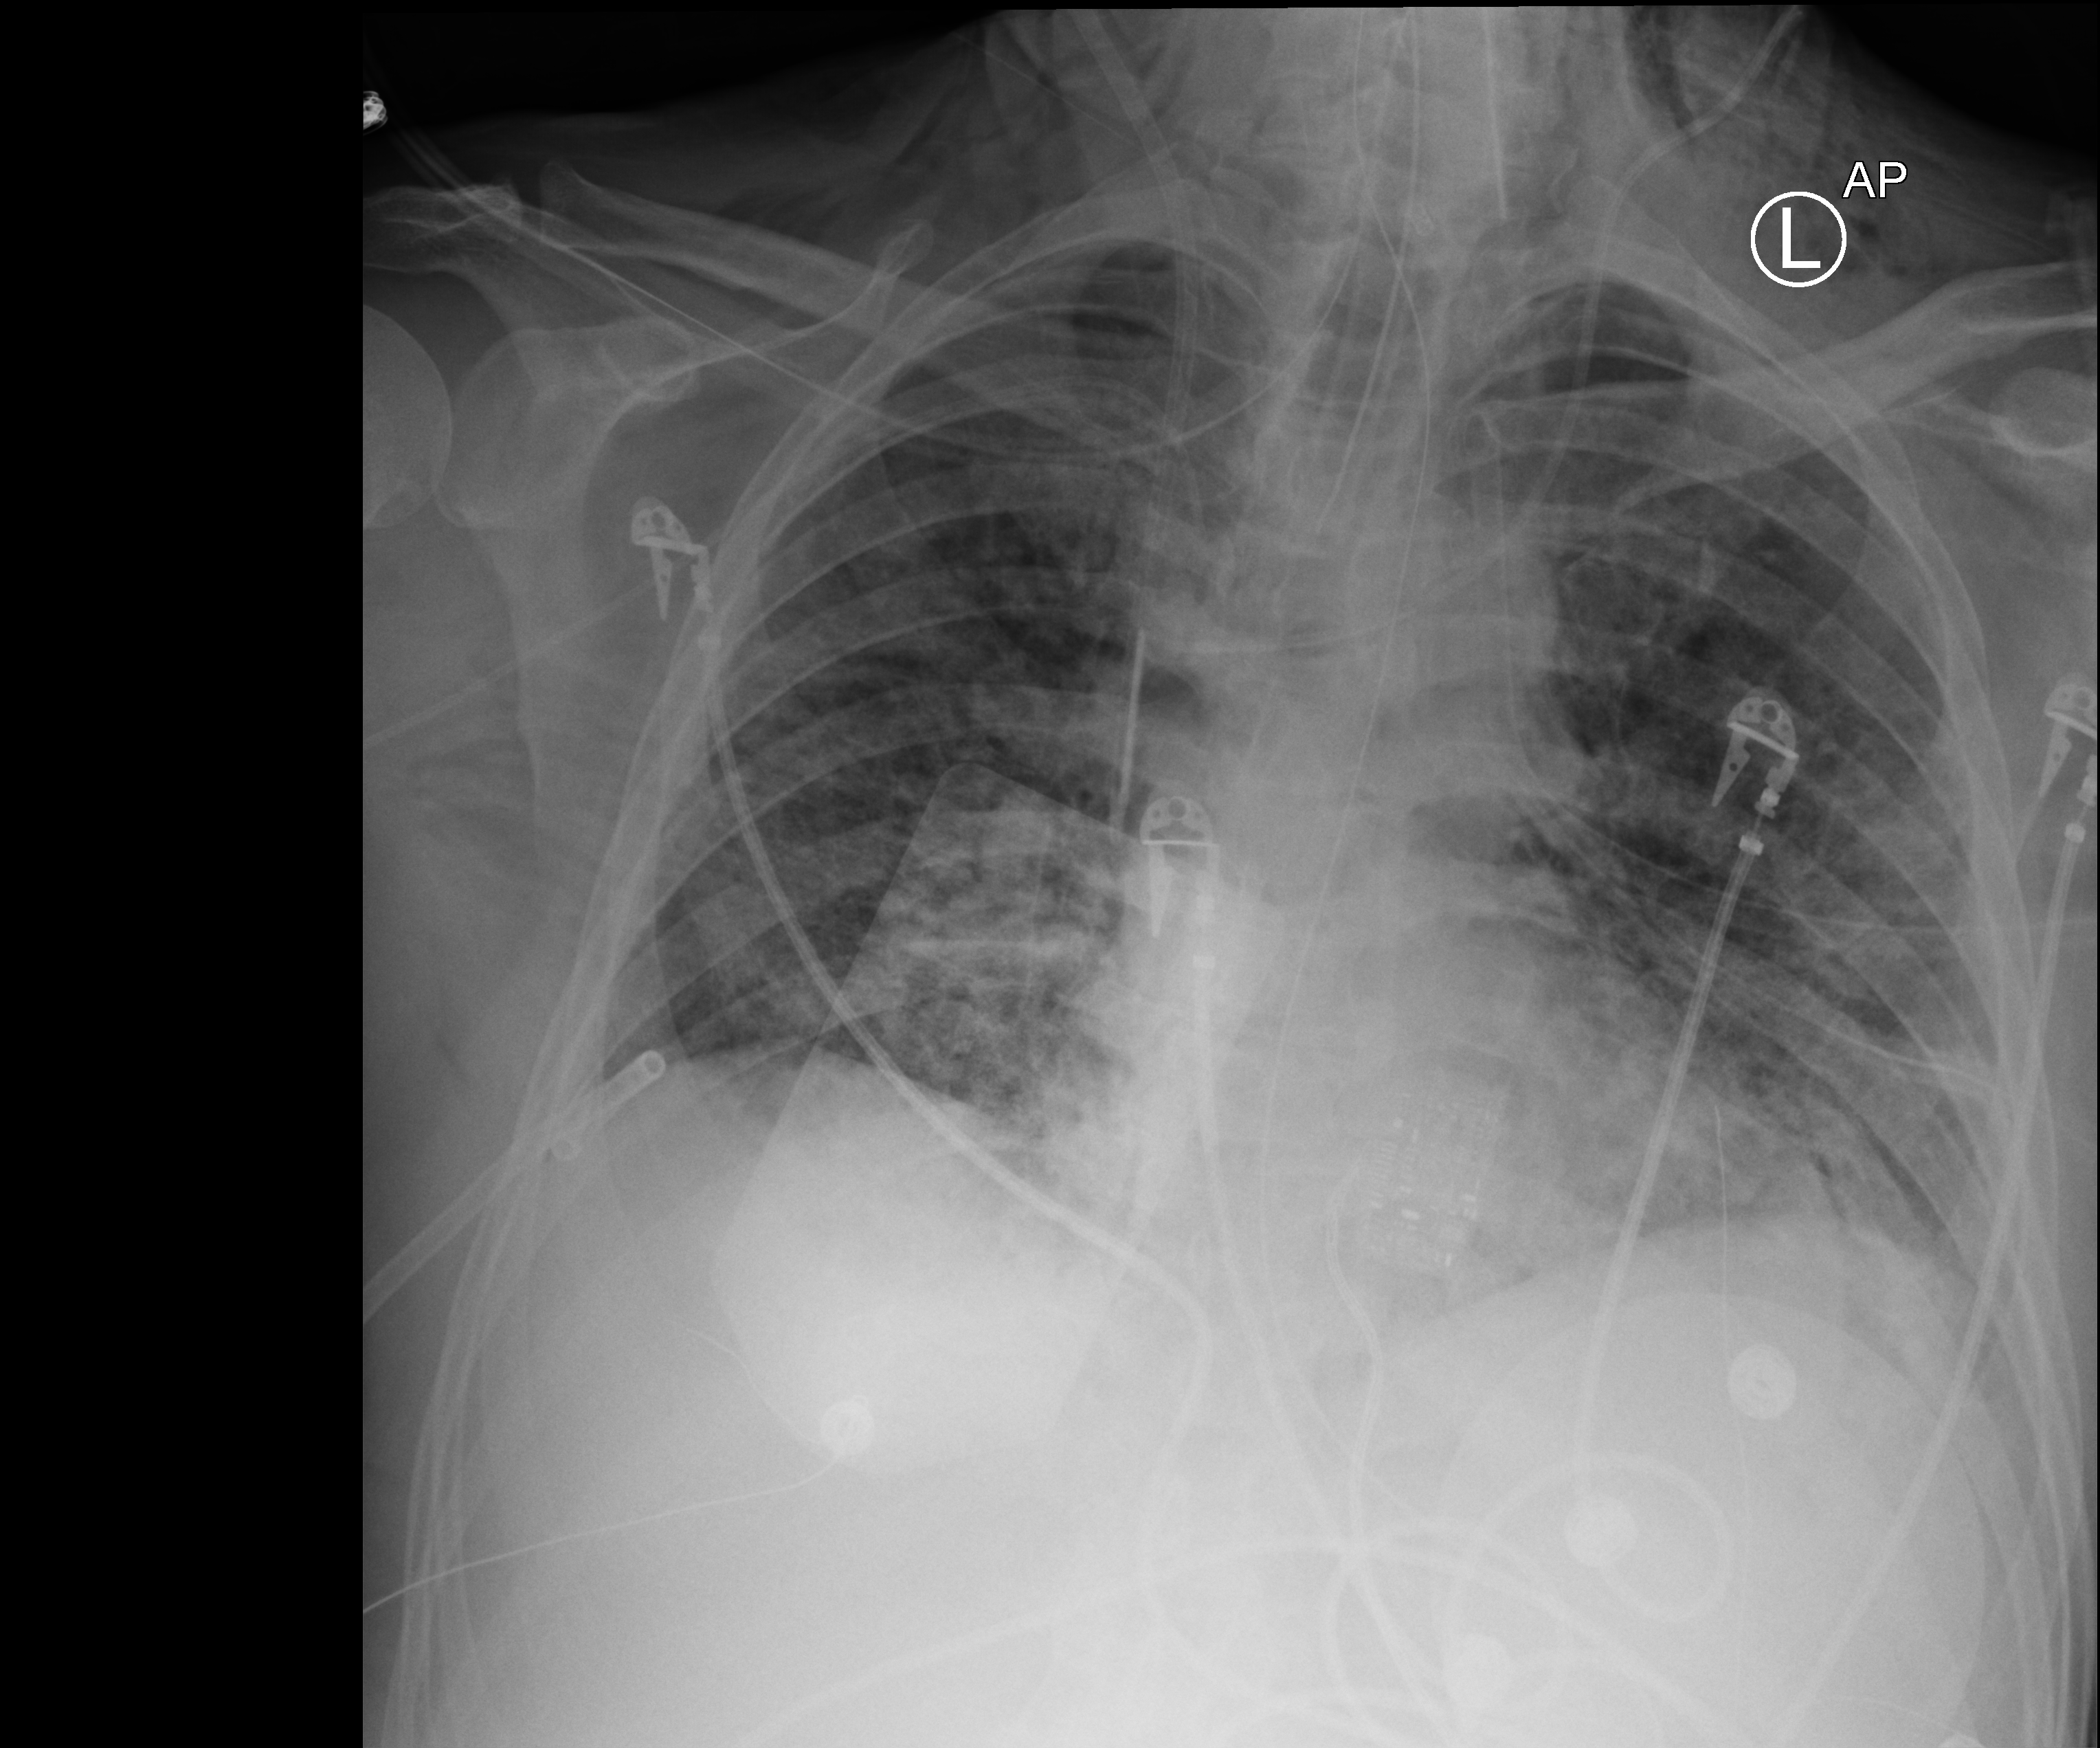
Portable chest radiograph. Male patient hospitalised with COVID-19, age 18–59 years.
Admission-level facts for this patient (not findings on this image; timing relative to this image not recorded): hypertension (admission record): no; other chronic lung disease (admission record): no; admitted to intensive care during this hospital stay: yes.